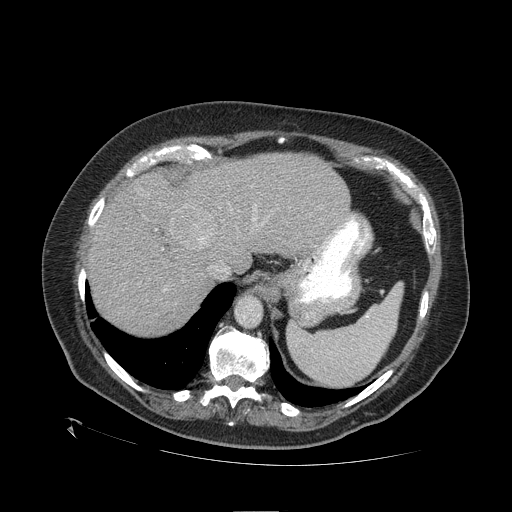
Contrast-enhanced abdominal CT (liver protocol), one axial slice. Slice 84 of 109 in the series (ordered by position). 120 kVp. One of 2 acquisitions stored at this slice position. Soft-tissue window (W 400 / L 40 HU). 2.5 mm slice thickness. 512 × 512 image matrix. Case-level facts recorded for this patient, not image findings: diagnosis: hepatocellular carcinoma (patient treated with transarterial chemoembolisation; whether this scan precedes or follows treatment is not stated here); TNM stage (as recorded): Stage-I; Child-Pugh class: A; tumour differentiation: no biopsy; tumour nodularity: uninodular.
Structures marked on this image (semi-automatically segmented with operator editing):
- liver parenchyma outside the tumour (the mass and vessels are separate outlines, so this box may not span the whole liver): bounding box <88,152,350,334> (left, top, right, bottom; pixels)
- mass: <168,203,221,250>
- liver vessels: <156,208,264,291>